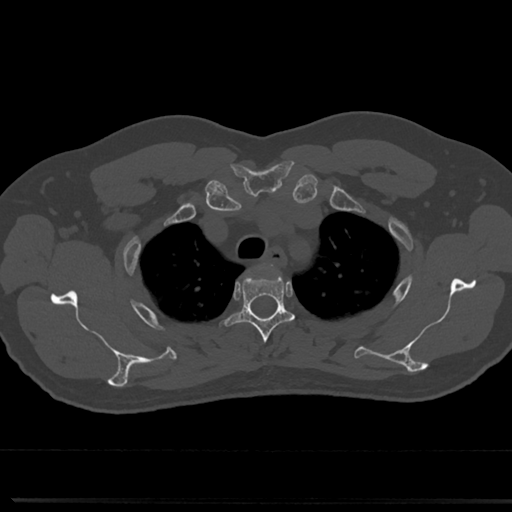
CT including the spine, one axial slice. Position 594 of 817 along the scan axis. Bone window (W 1800 / L 400 HU). 0.5 mm slice thickness. 512 × 512 image matrix, field of view 355 × 355 mm. Male patient, age 61 years. From the clinical record (not read from this slice): primary cancer: prostate.
Annotated regions visible in this slice (semi-automatically segmented with operator editing):
- T3 vertebra: bounding box [x1, y1, x2, y2] px = [233, 266, 292, 349]